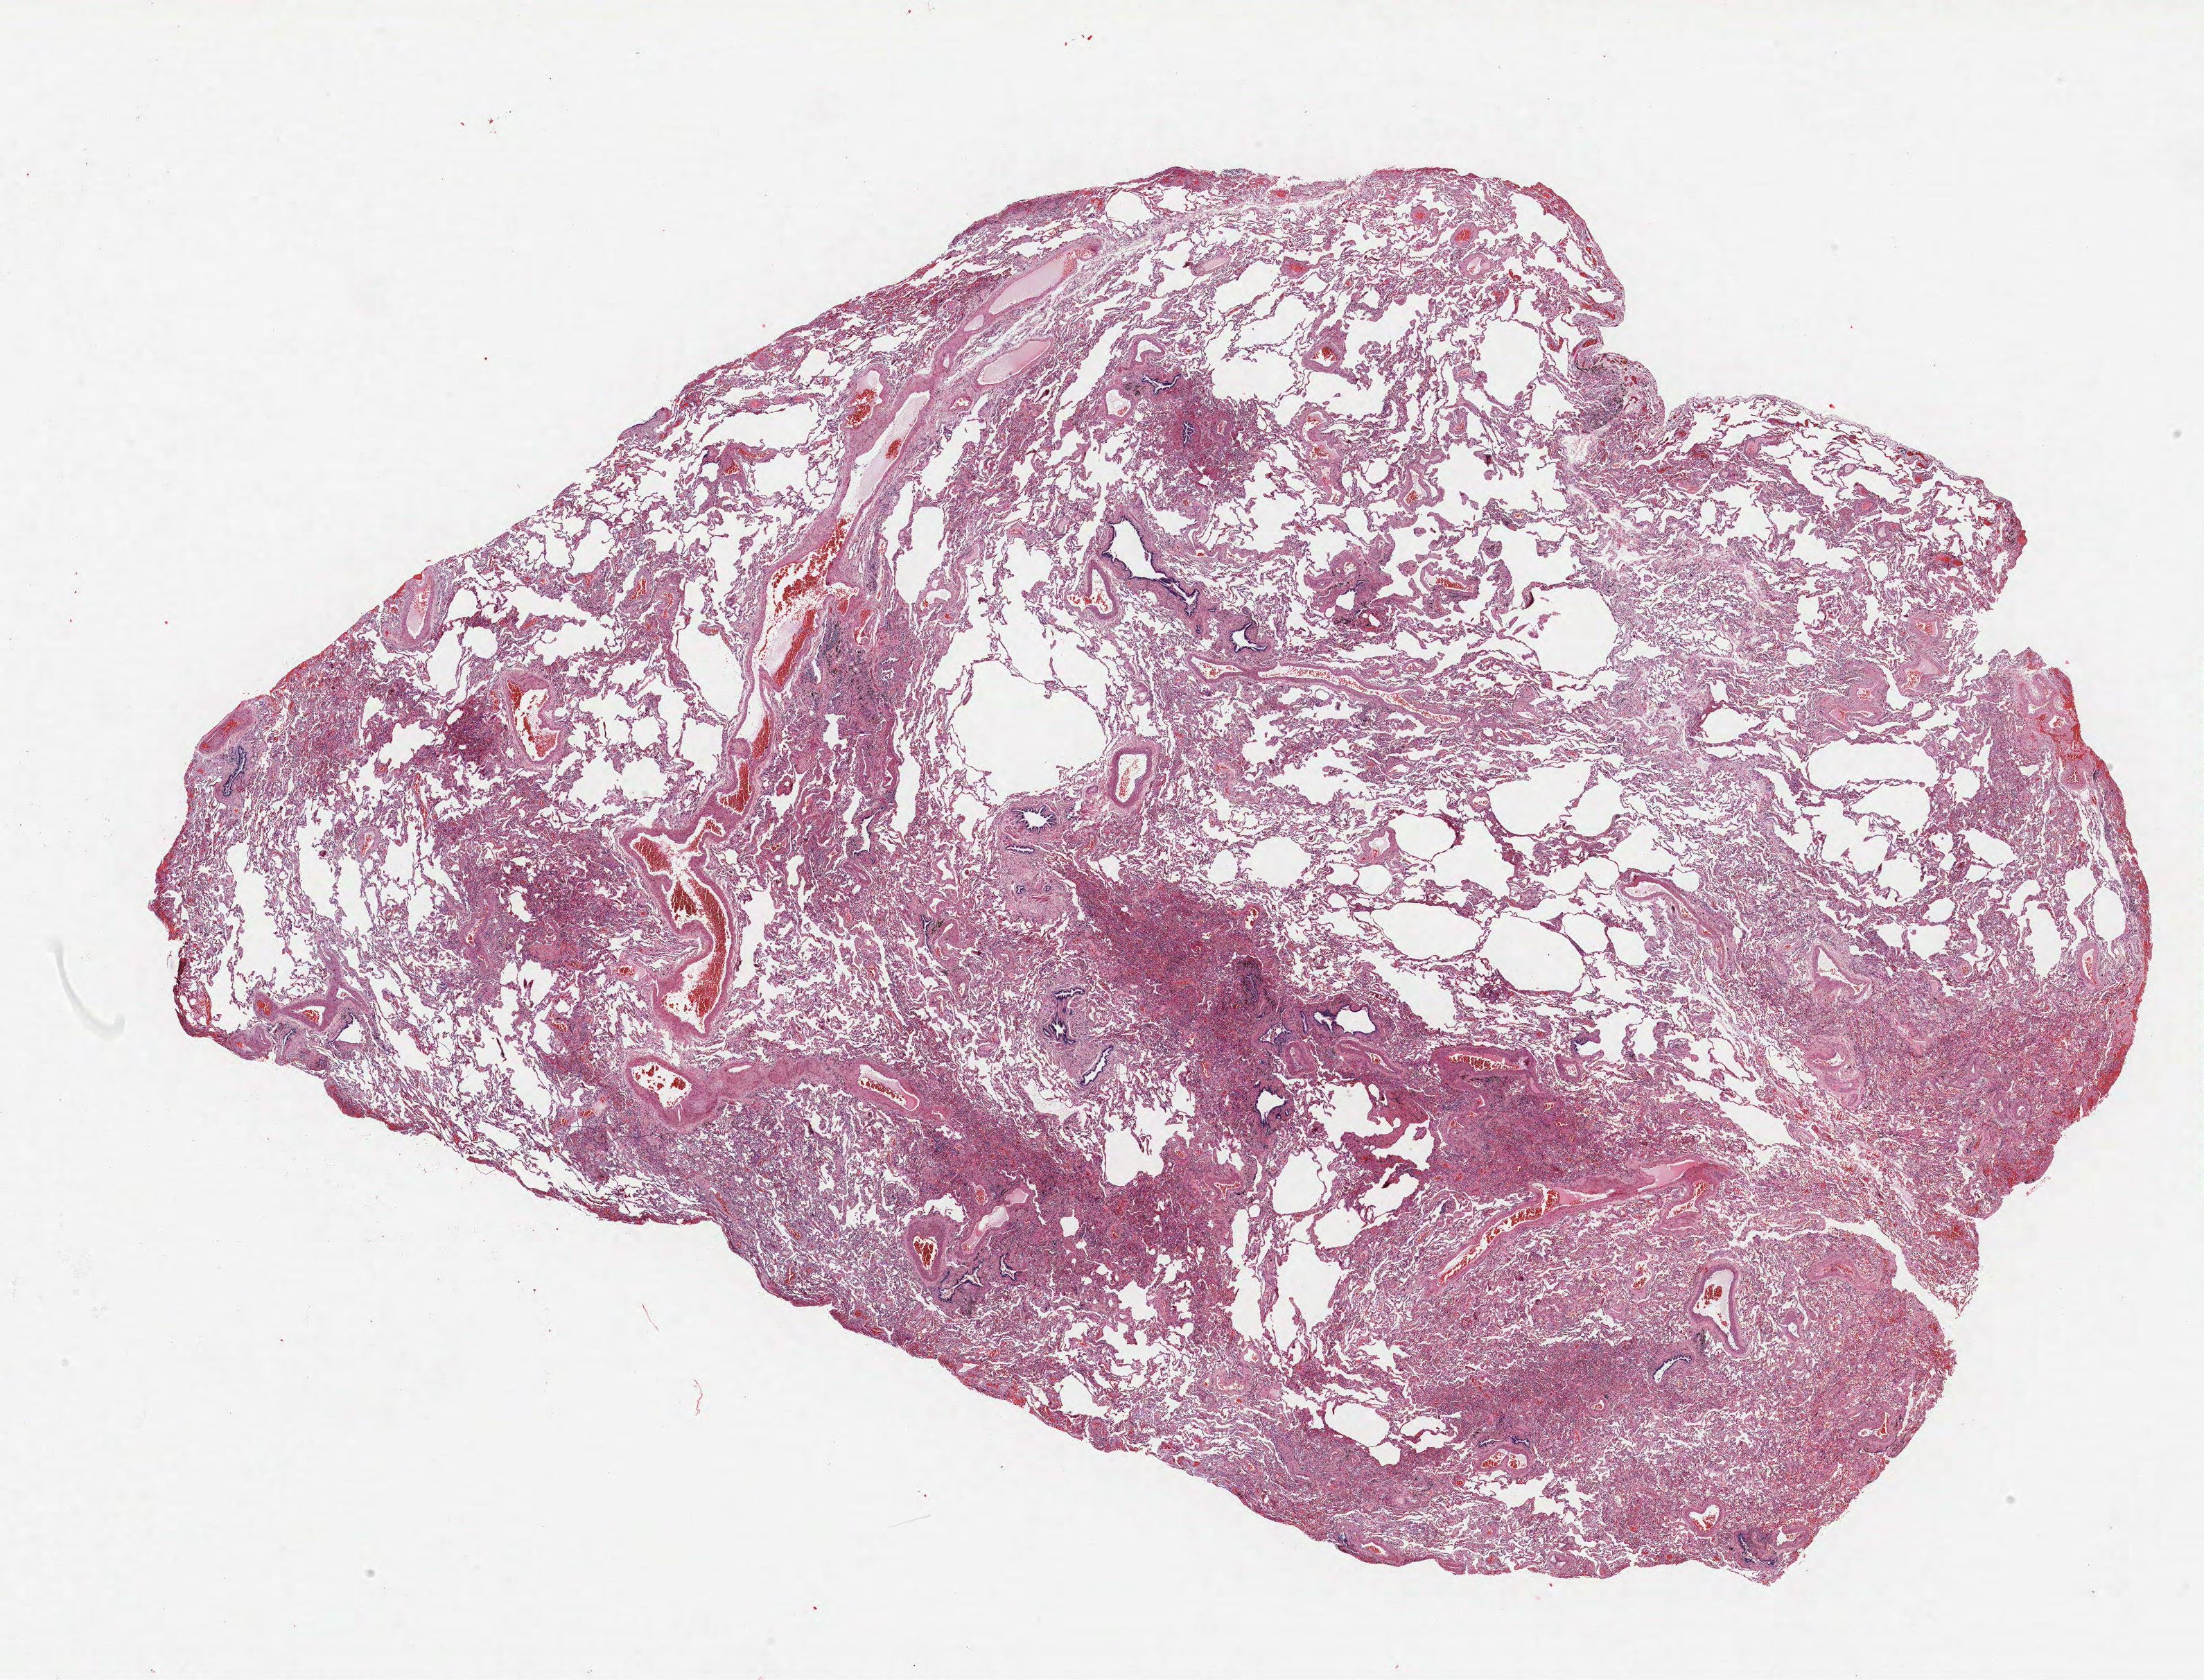
Whole-slide histology image, H&E-stained — a low-resolution overview of the entire scanned area, about 25.4 x 19.4 mm, FFPE section, lung. Male, age 66 at enrolment. Former smoker at enrolment. Grade: poorly differentiated (G3).
Tumour size (pathology): 33 mm. Participant's lung-cancer diagnosis: Adenocarcinoma, NOS (ICD-O-3 8140/3). Stage (AJCC 6th edition): IIB. Primary tumour location (clinical record): right upper lobe.